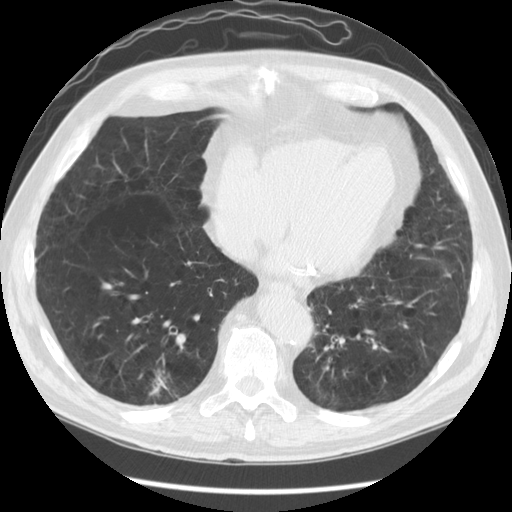
Low-dose screening chest CT, axial slice; baseline screening round; lung window (W 1500 / L -600 HU); standard (soft-tissue) reconstruction kernel (STANDARD); slice 95 of 141 in the series; 512 × 512 image matrix. Male, age 67 years at enrolment. Former smoker at enrolment.
Lesion marked by an expert reader, bounding box [x1, y1, x2, y2] px = [120, 356, 188, 418]. The screening reader recorded 2 non-calcified nodules or masses ≥4 mm on this exam (right lower lobe, right lower lobe); which of them this box marks is not recorded. Later outcome: lung cancer diagnosed 78 days after this screen — squamous cell carcinoma, NOS, right lower lobe, moderately differentiated (G2), stage IA (AJCC 6th edition), 23 mm at pathology.